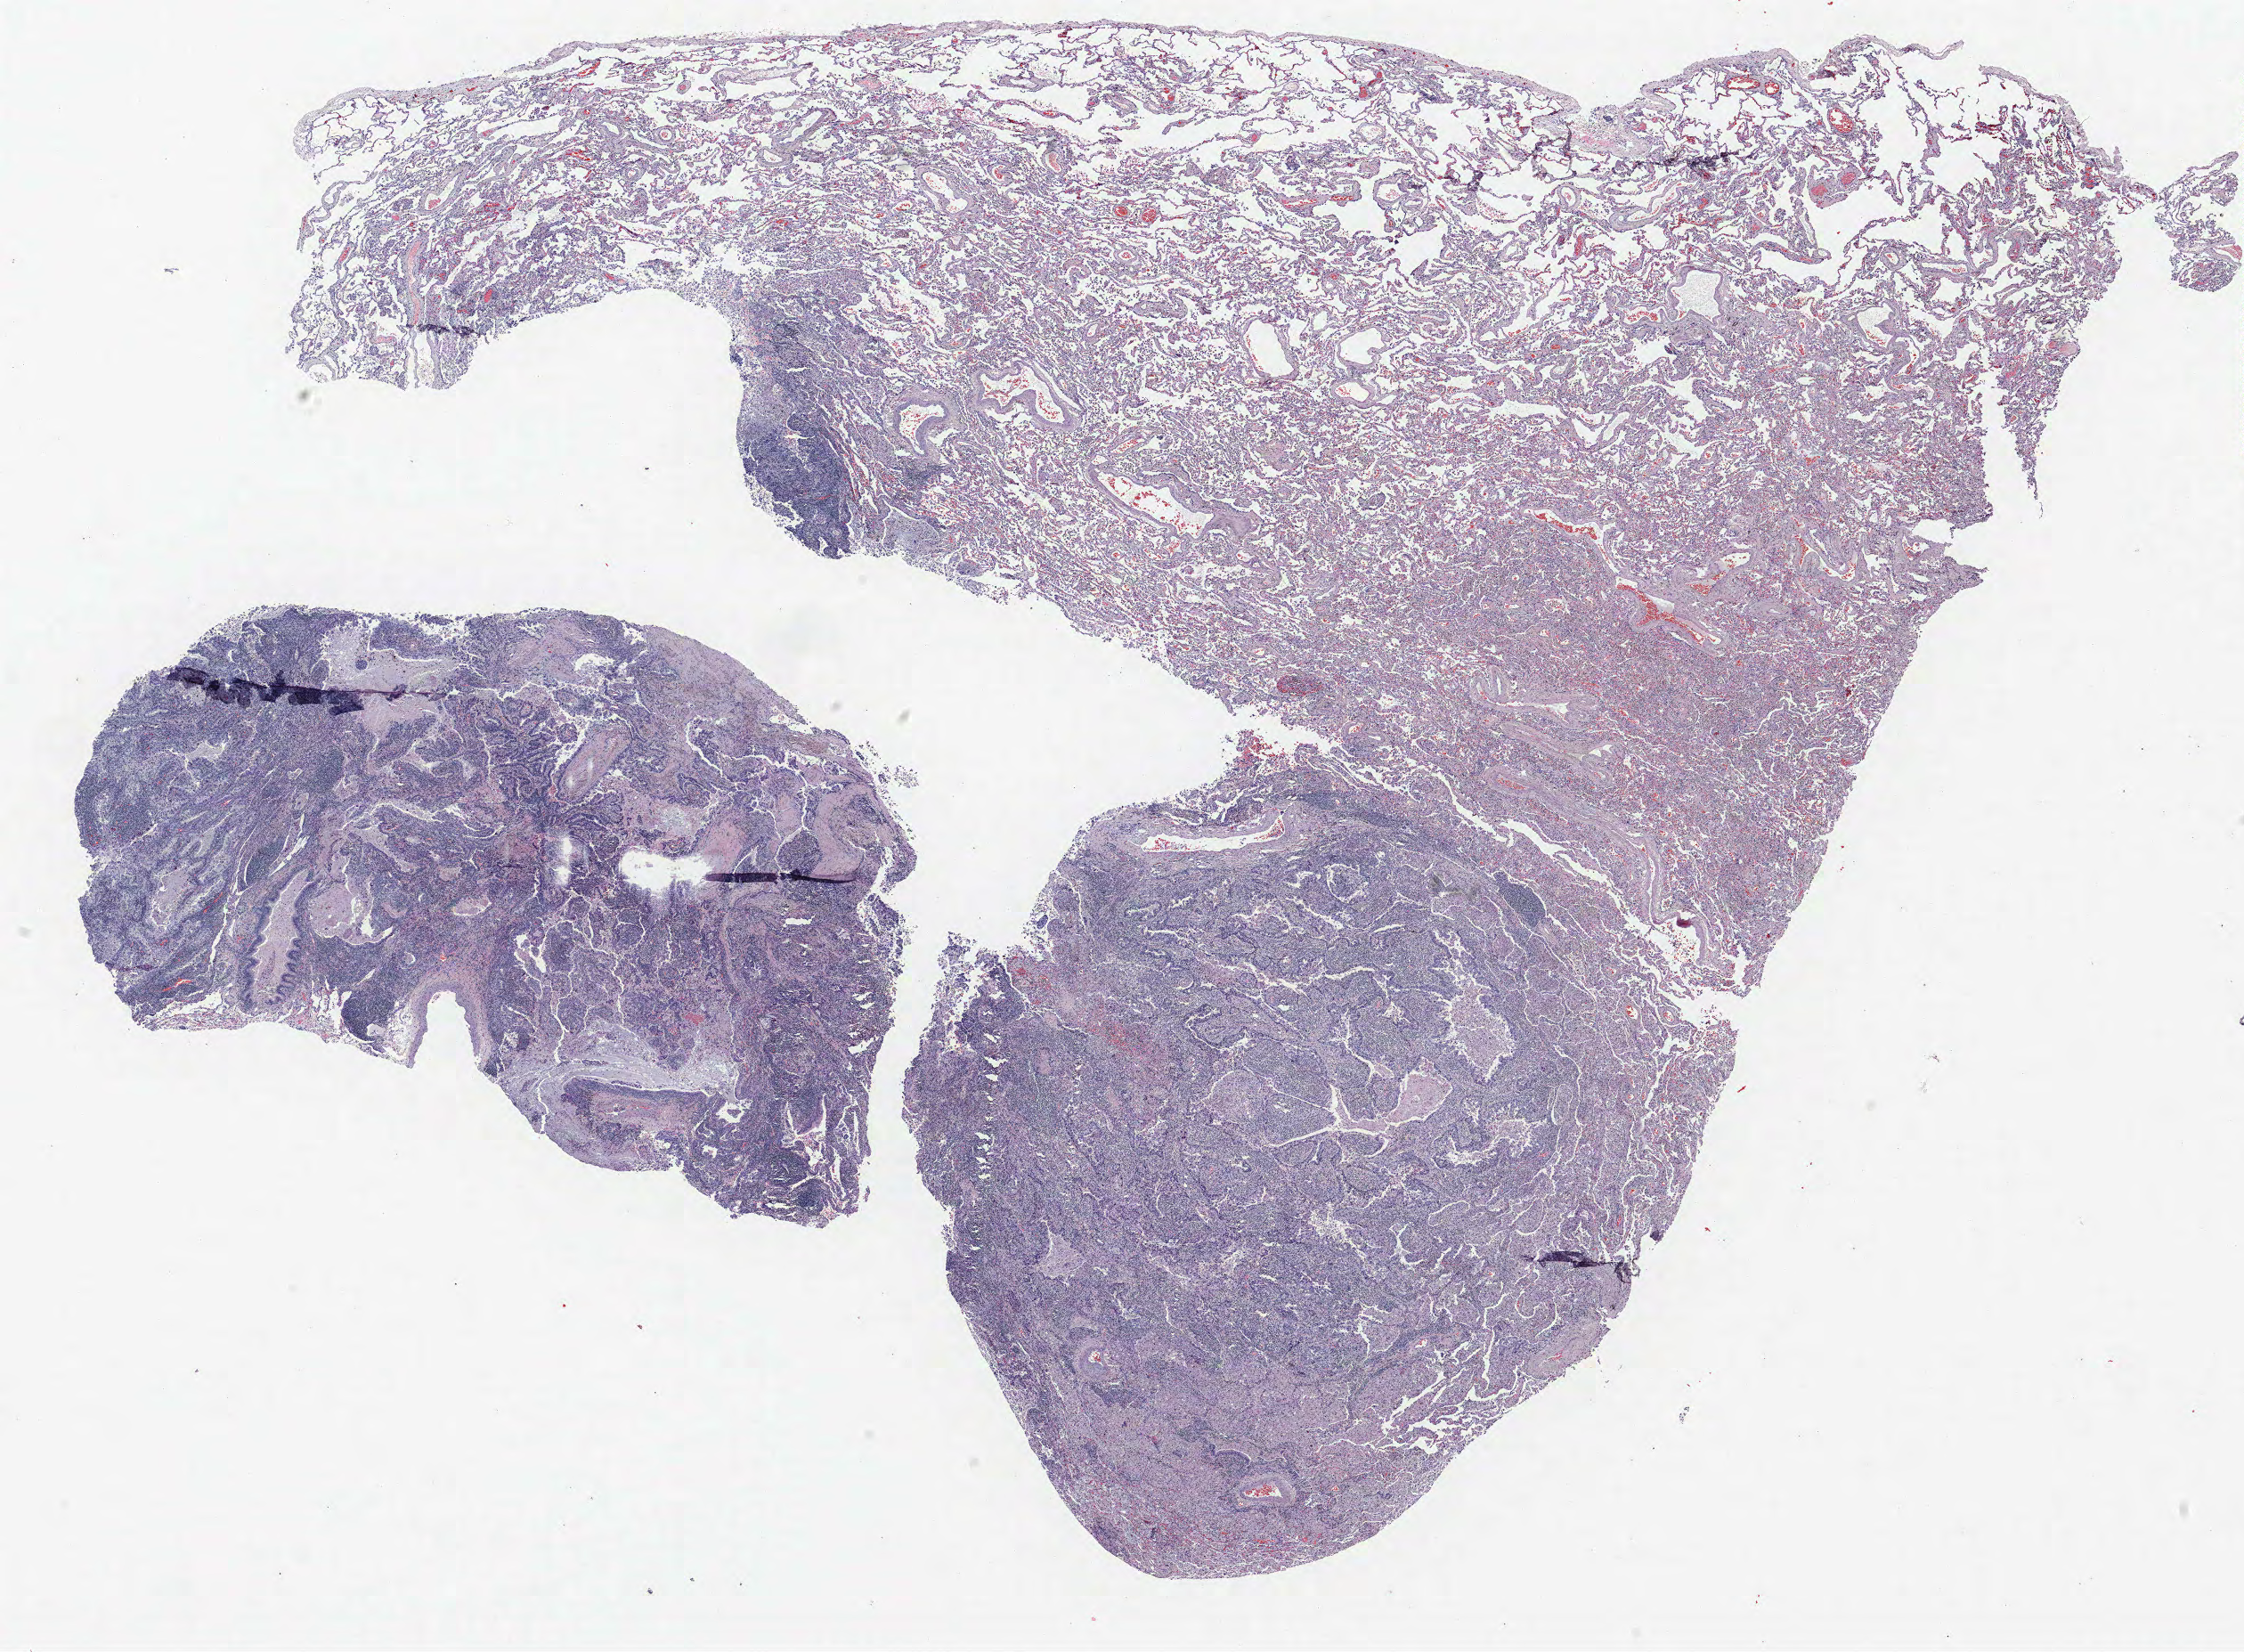
Whole-slide histology image, Hematoxylin and eosin (H&E) stained, shown as a low-resolution overview of the whole scanned area (about 20.2 x 14.8 mm), FFPE section, lung. Female, age 61 at enrolment. Current smoker at enrolment. Grade: moderately differentiated (G2).
Primary tumour location (clinical record): left lower lobe. Participant's lung-cancer diagnosis: Adenocarcinoma, NOS. Stage (AJCC 6th edition): IA. Tumour size (pathology): 18 mm.